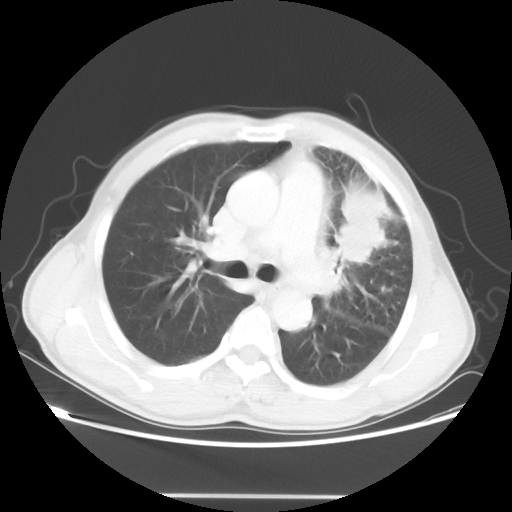
Chest CT, one axial slice. Slice 33 of 55 in the series (ordered by position). Reconstruction kernel STANDARD. 100 kVp. Lung window (W 1500 / L -600 HU). 5 mm slice thickness. 512 × 512 image matrix. Male patient, age 60 years. From the clinical record (not read from this slice): clinical TNM (as recorded): T3 N3 M0.
Structures marked on this image (bounding box drawn by a radiologist):
- lung tumour (recorded histology: adenocarcinoma): bounding box [x1, y1, x2, y2] px = [331, 180, 396, 272]